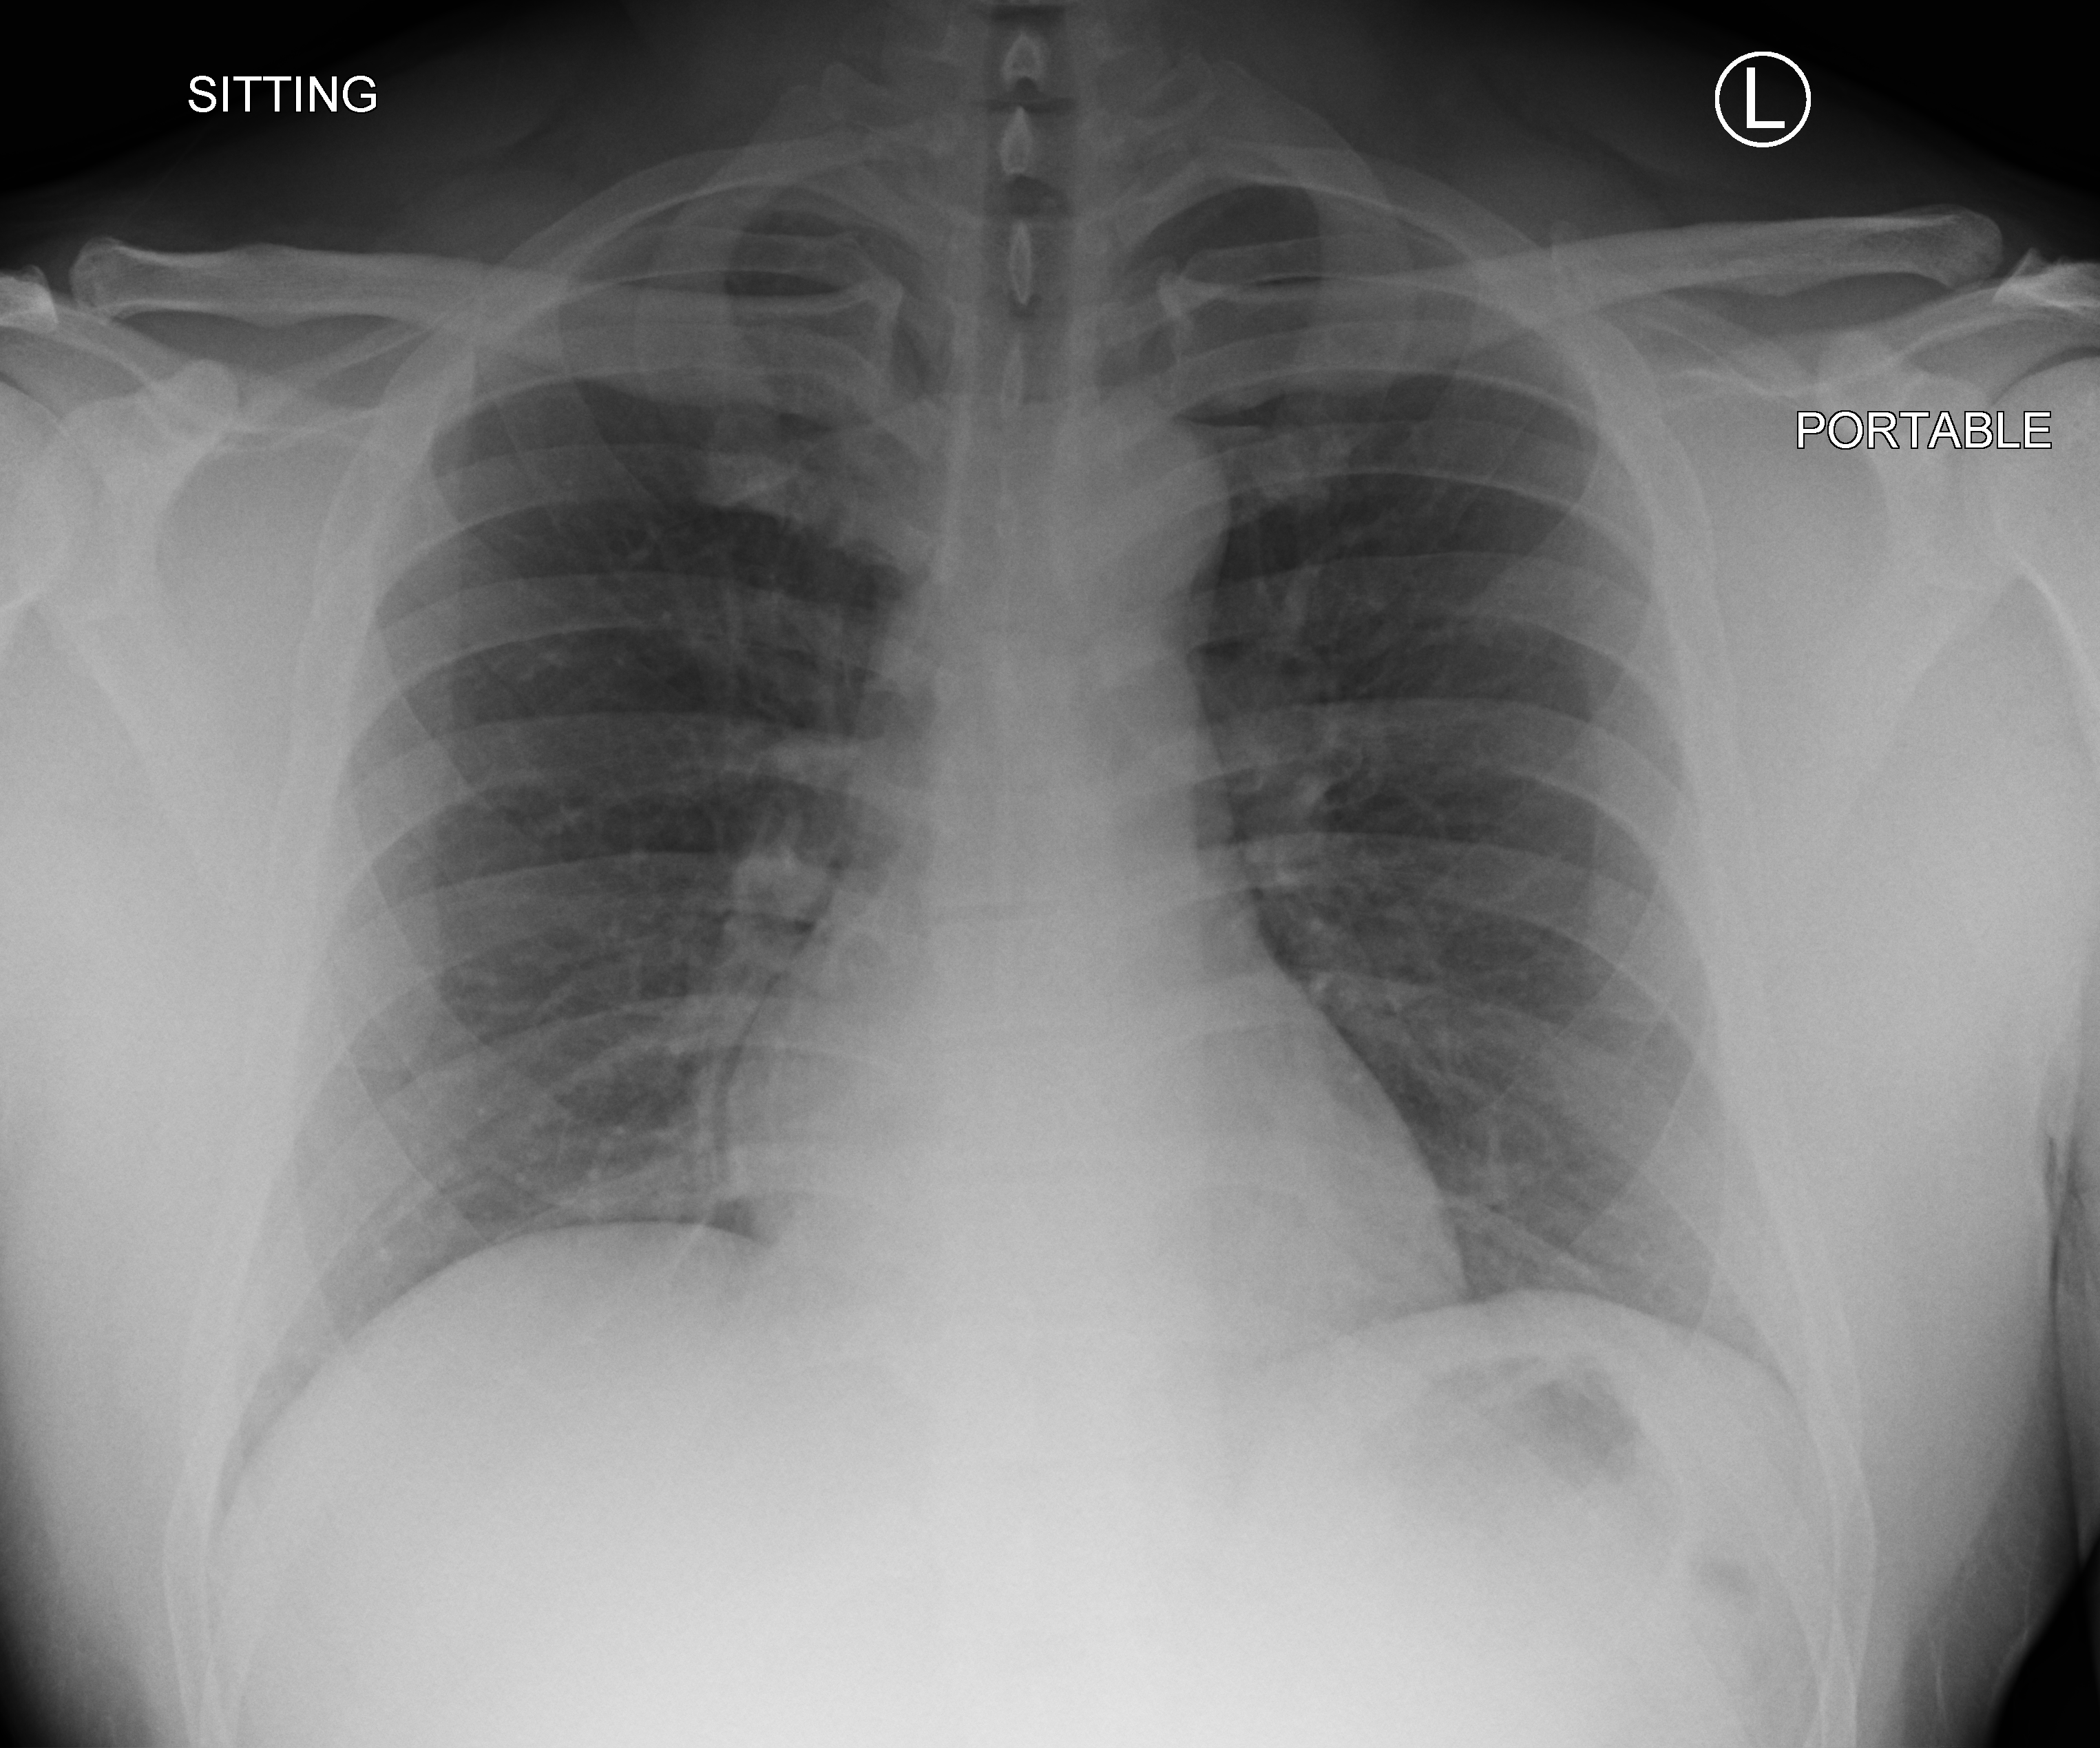
Bedside chest radiograph (computed radiography). Patient hospitalised with COVID-19; male, aged 18–59 years.
From the hospital-stay record, not from the radiograph (when in the stay this image was taken is not recorded): COPD (admission record): no; mechanically ventilated during this hospital stay: no.